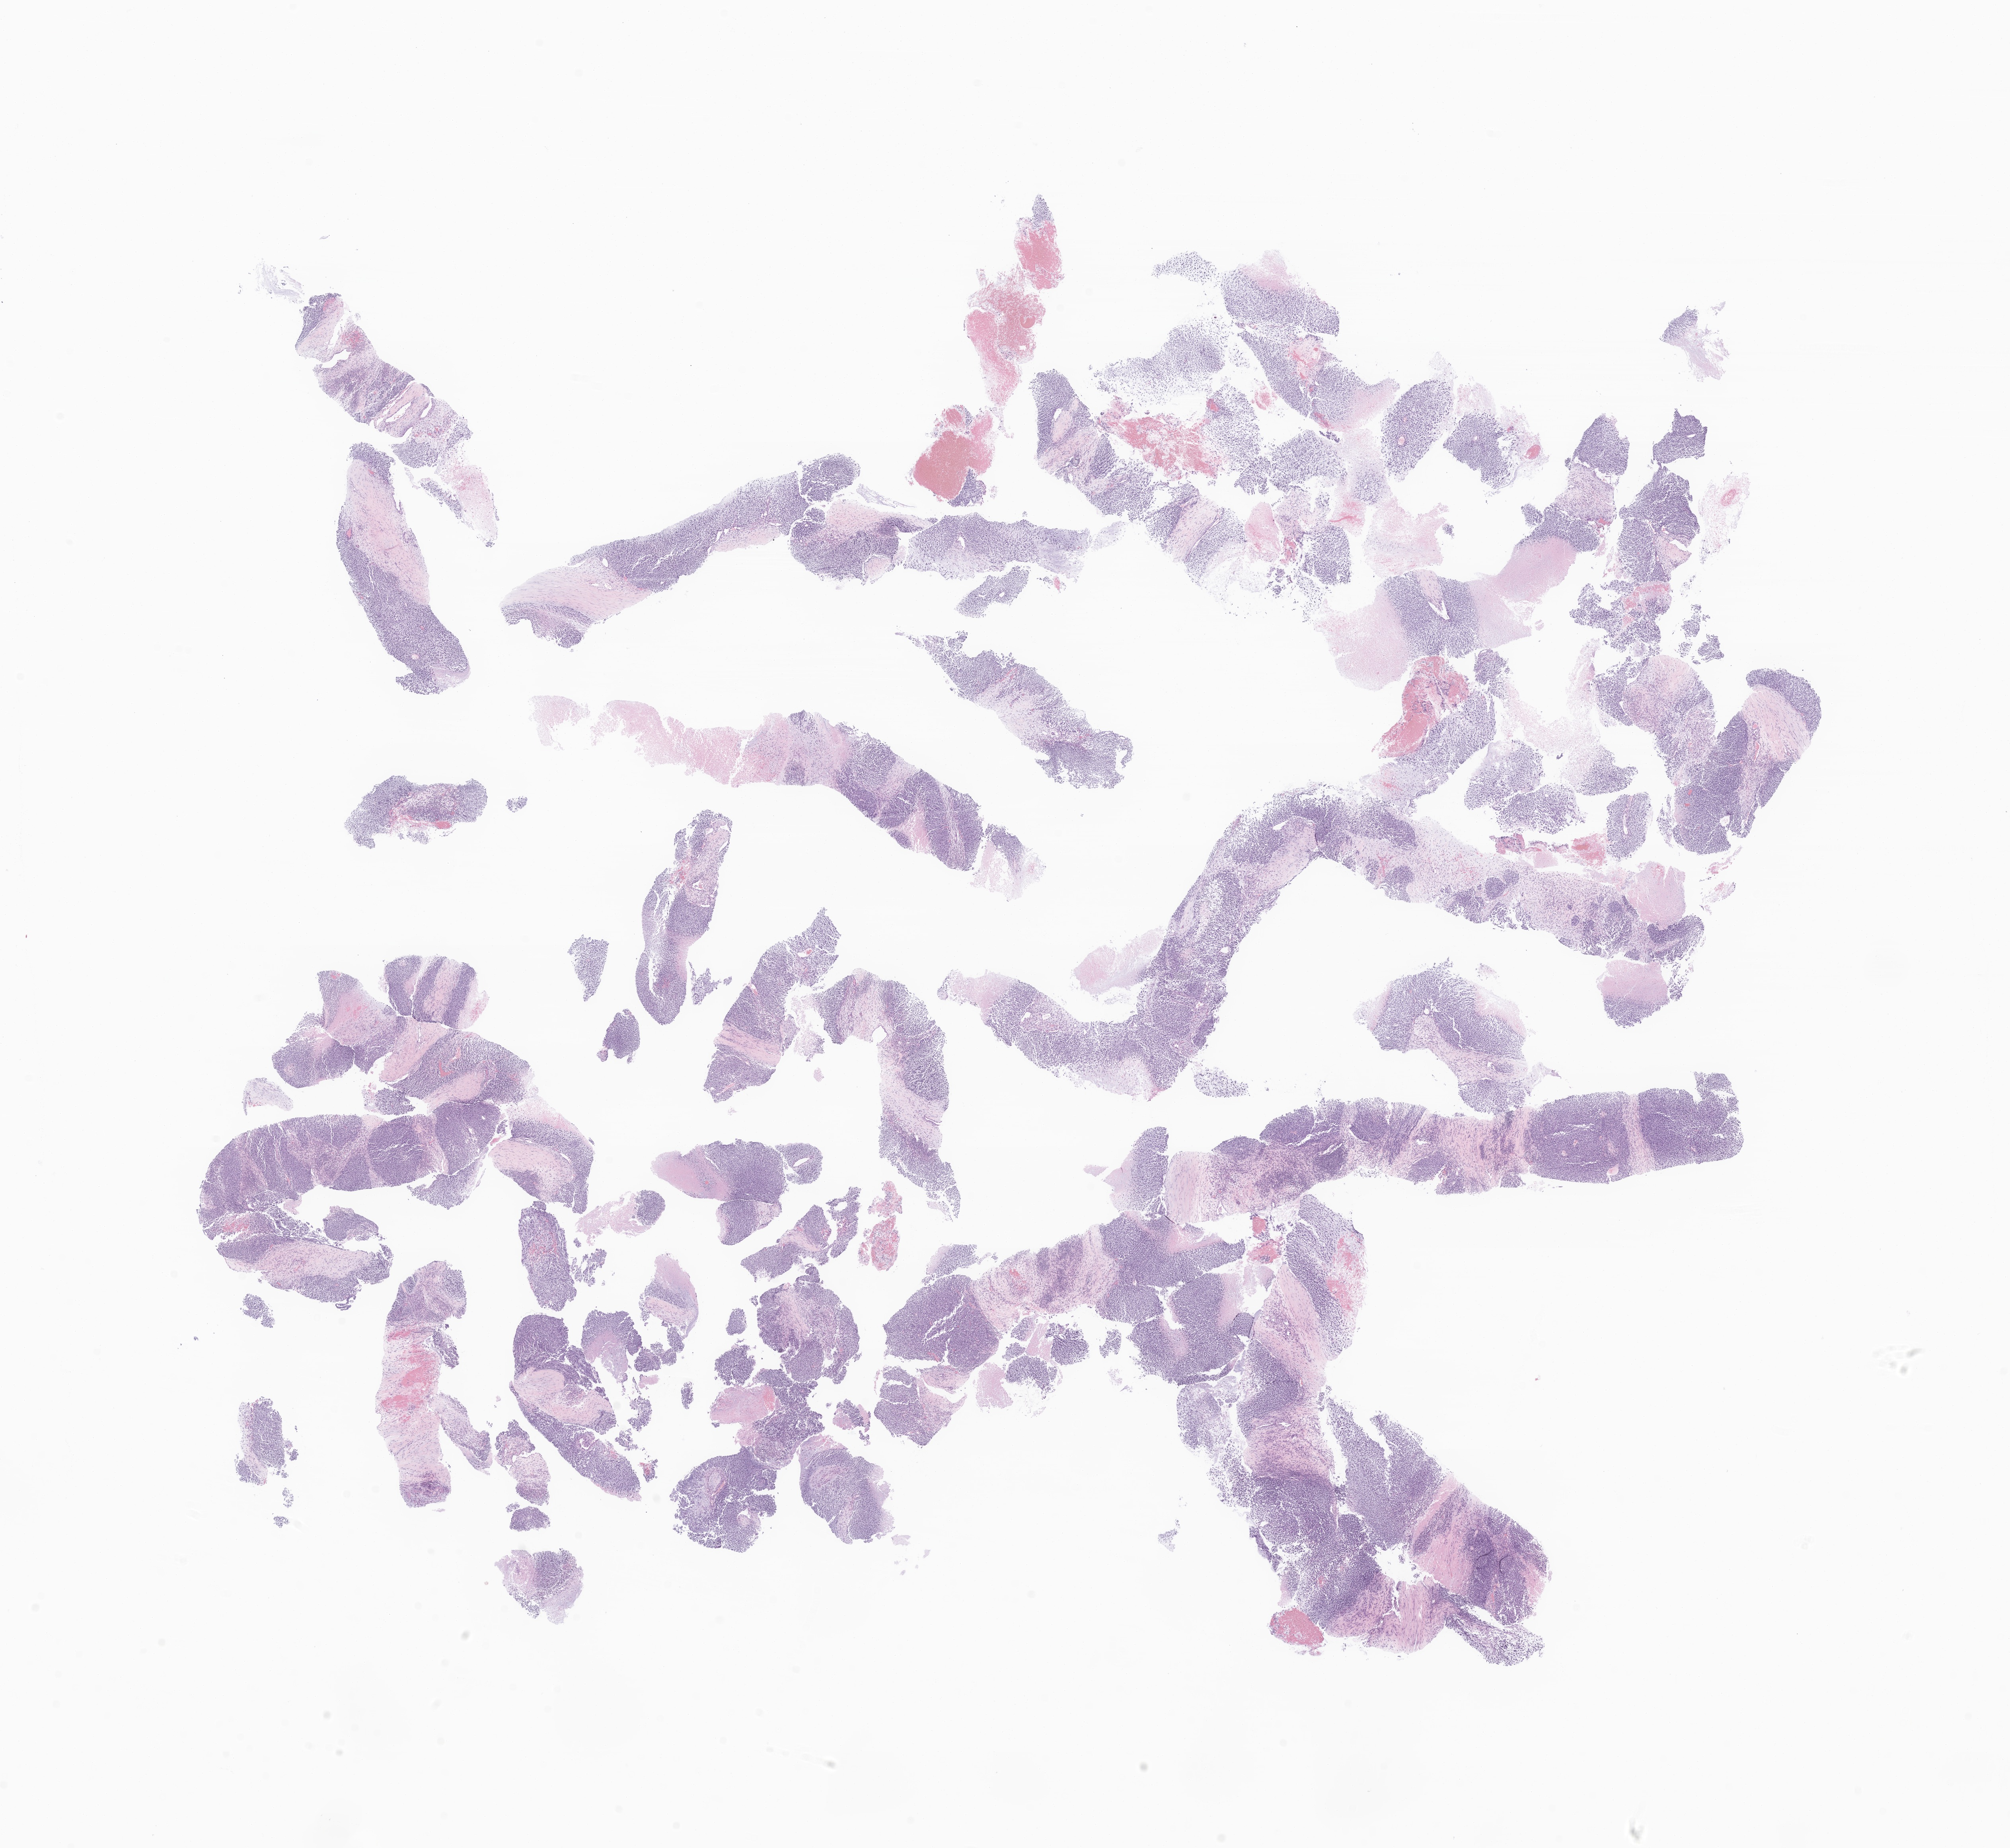
Whole-slide image, hematoxylin and eosin (H&E) stain of tumor tissue from the soft tissue of lower extremity — low-resolution overview of the scanned area, about 21.3 x 19.6 mm, formalin-fixed, paraffin-embedded (FFPE) tissue. Patient: male, age 175 months.
* diagnosis (ICD-O-3 morphology term): Undifferentiated sarcoma
* tissue or organ of origin (case record): connective, subcutaneous and other soft tissues of lower limb and hip